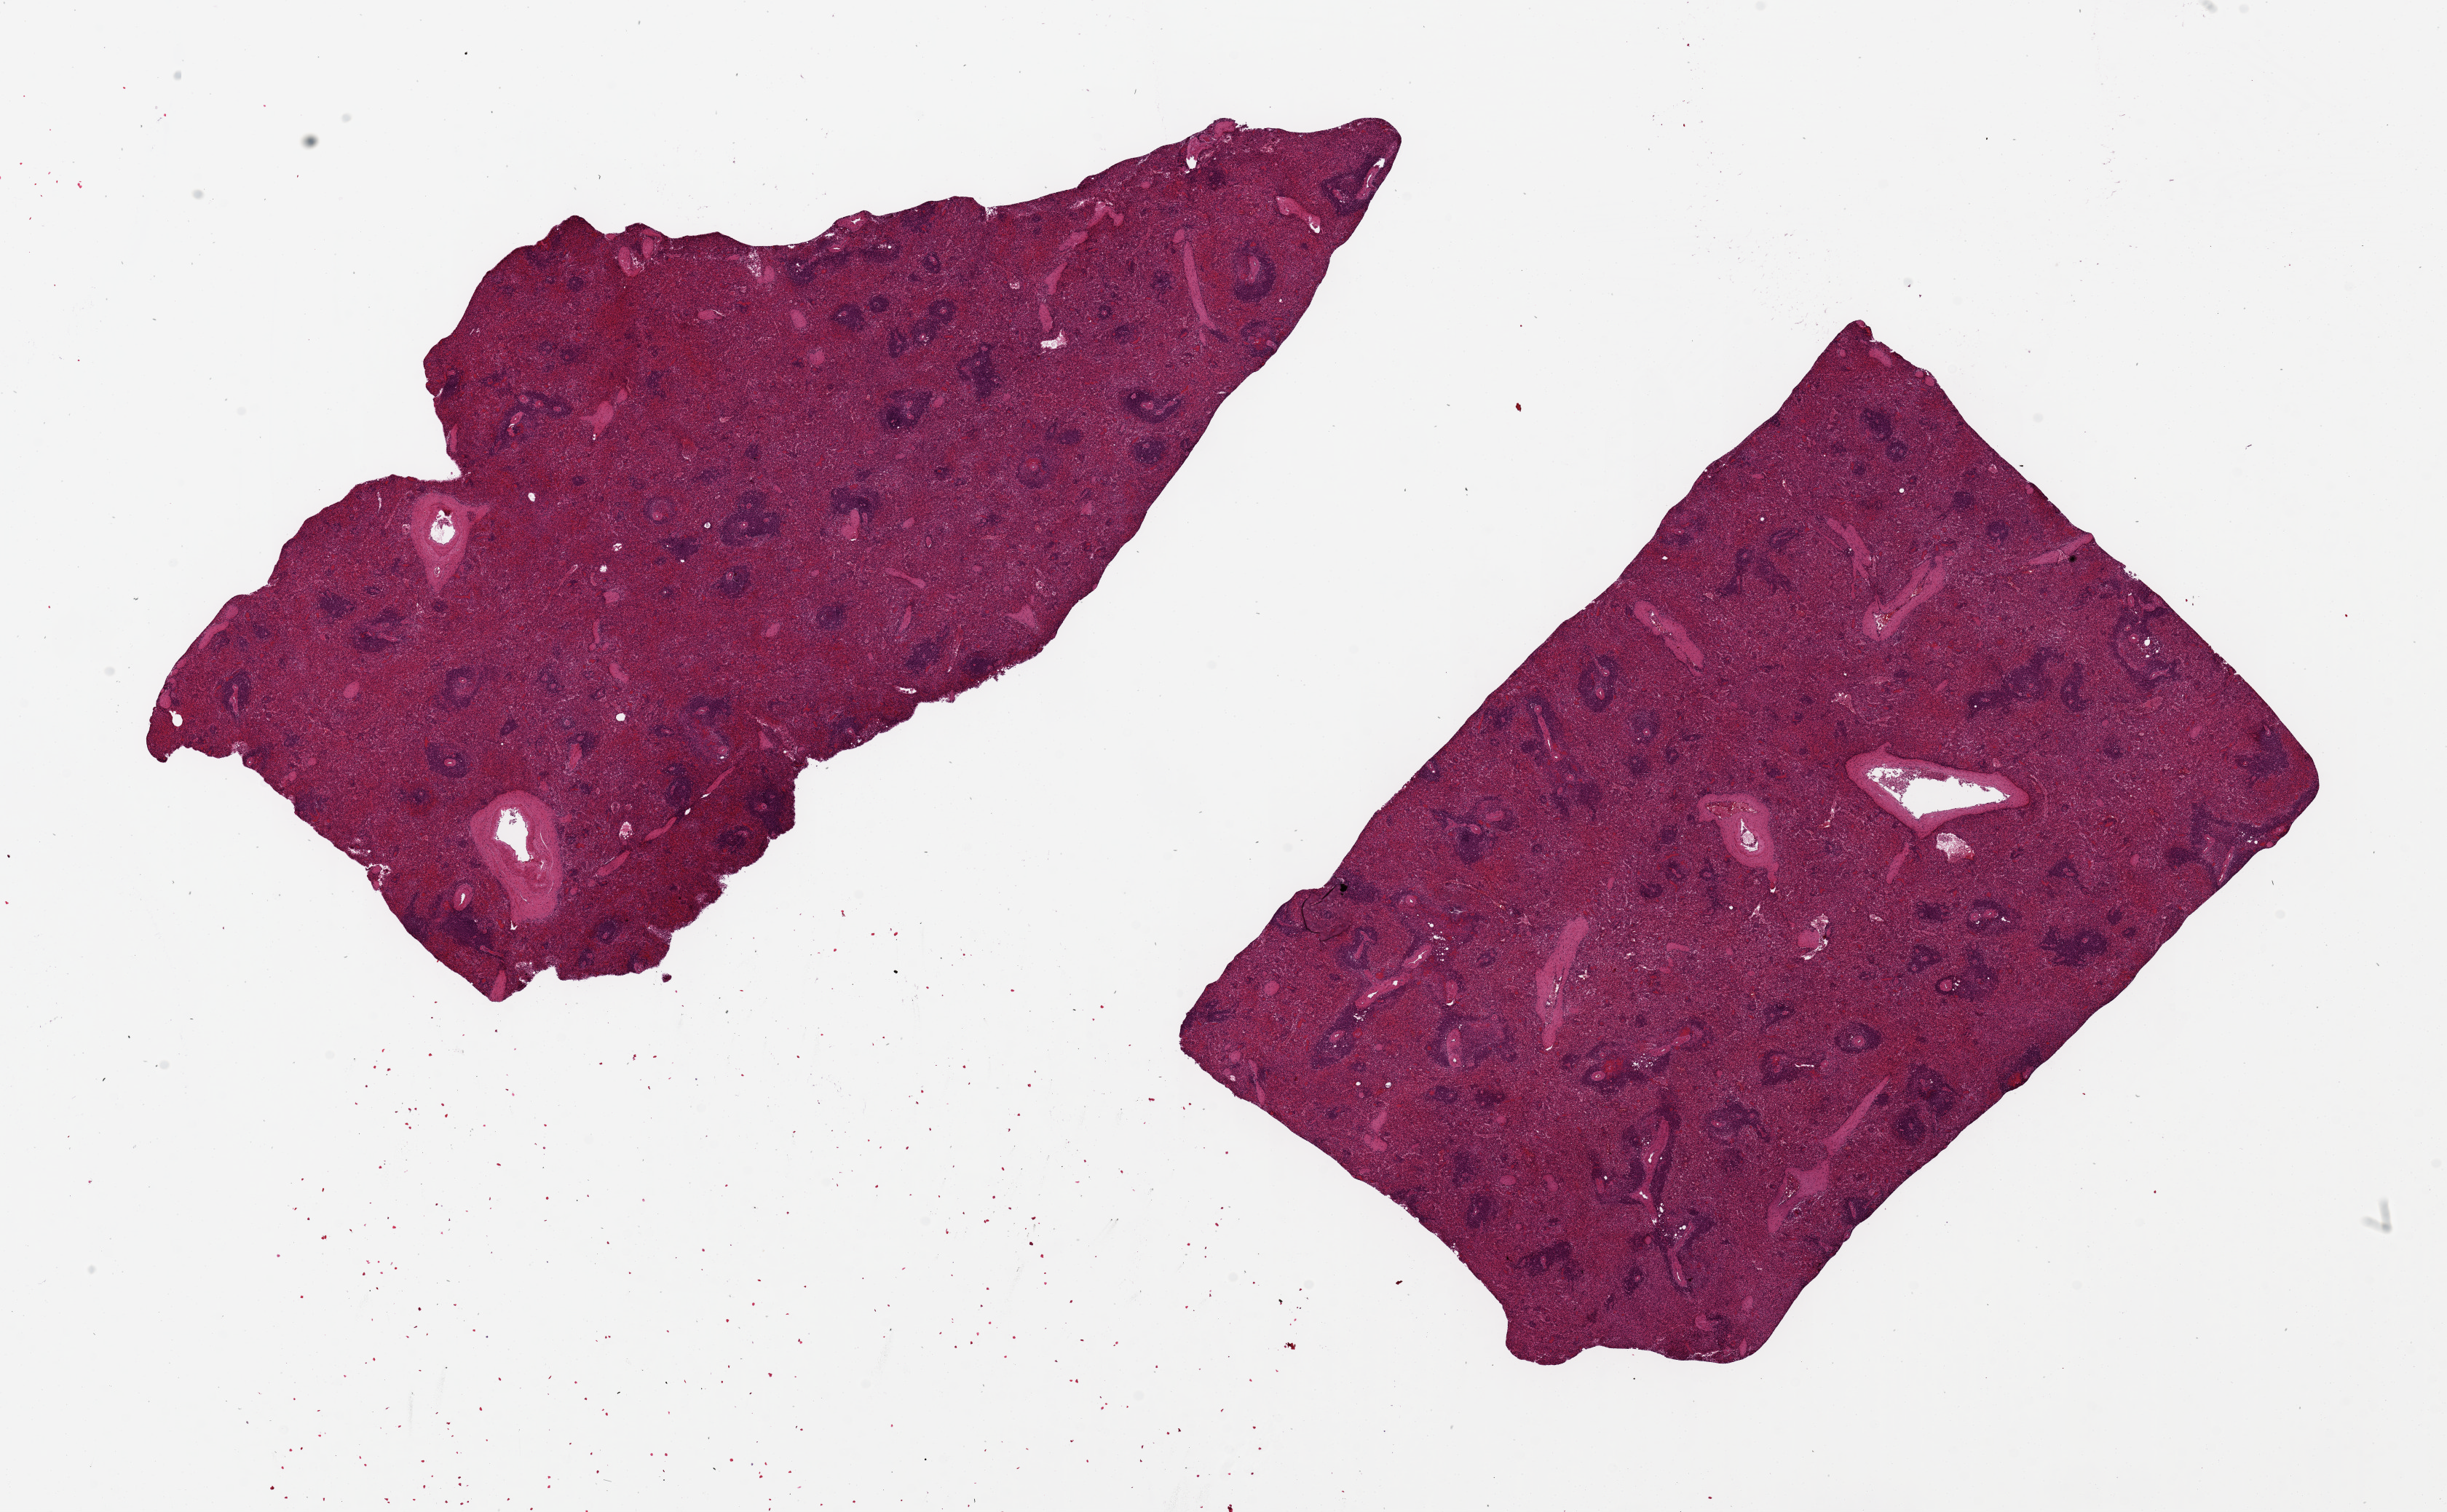
Digitized H&E-stained section — low-resolution overview of the scanned area, about 26.6 x 16.4 mm, PAXgene-fixed, paraffin-embedded tissue, target tissue: spleen, donor tissue sample. Male donor.
Reviewer comment on this tissue sample: 2 pieces ~12x7mm, moderate congestion.